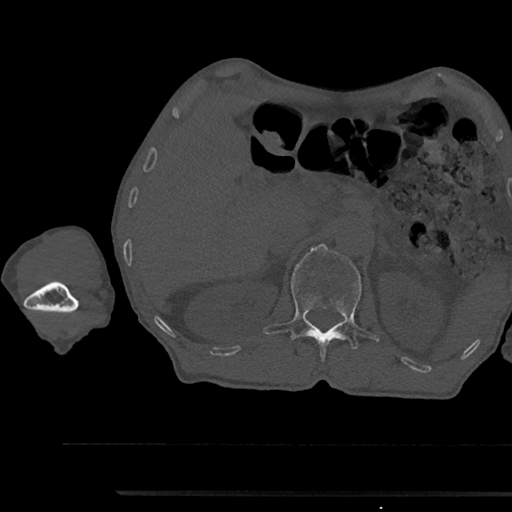
CT including the spine, one axial slice. Position 644 of 797 along the scan axis. Reconstruction kernel Br40s/3. Bone window (W 1800 / L 400 HU). 512 × 512 image matrix. Patient: male, 79 years. From the clinical record (not read from this slice): primary cancer: prostate.
Outlined on this slice (semi-automatically segmented with operator editing):
- L1 vertebra: bounding box [x1, y1, x2, y2] px = [264, 243, 378, 359]